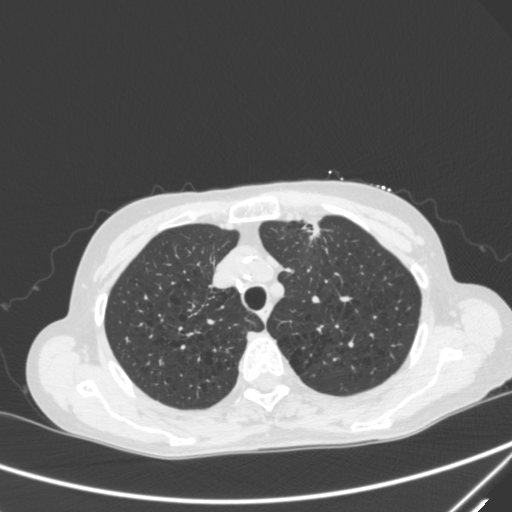
Chest CT, one axial slice; slice 237 of 300 in the series (ordered by position); lung window (W 1500 / L -600 HU); 512 × 512 image matrix, field of view 350 × 350 mm. Female patient, age 71 years. Case-level facts recorded for this patient, not image findings: clinical TNM (as recorded): T1c N0 M0; histopathological grade: G2-3.
Outlined on this slice (bounding box drawn by a radiologist):
- lung tumour (recorded histology: adenocarcinoma): bounding box [x1, y1, x2, y2] px = [298, 215, 325, 244]